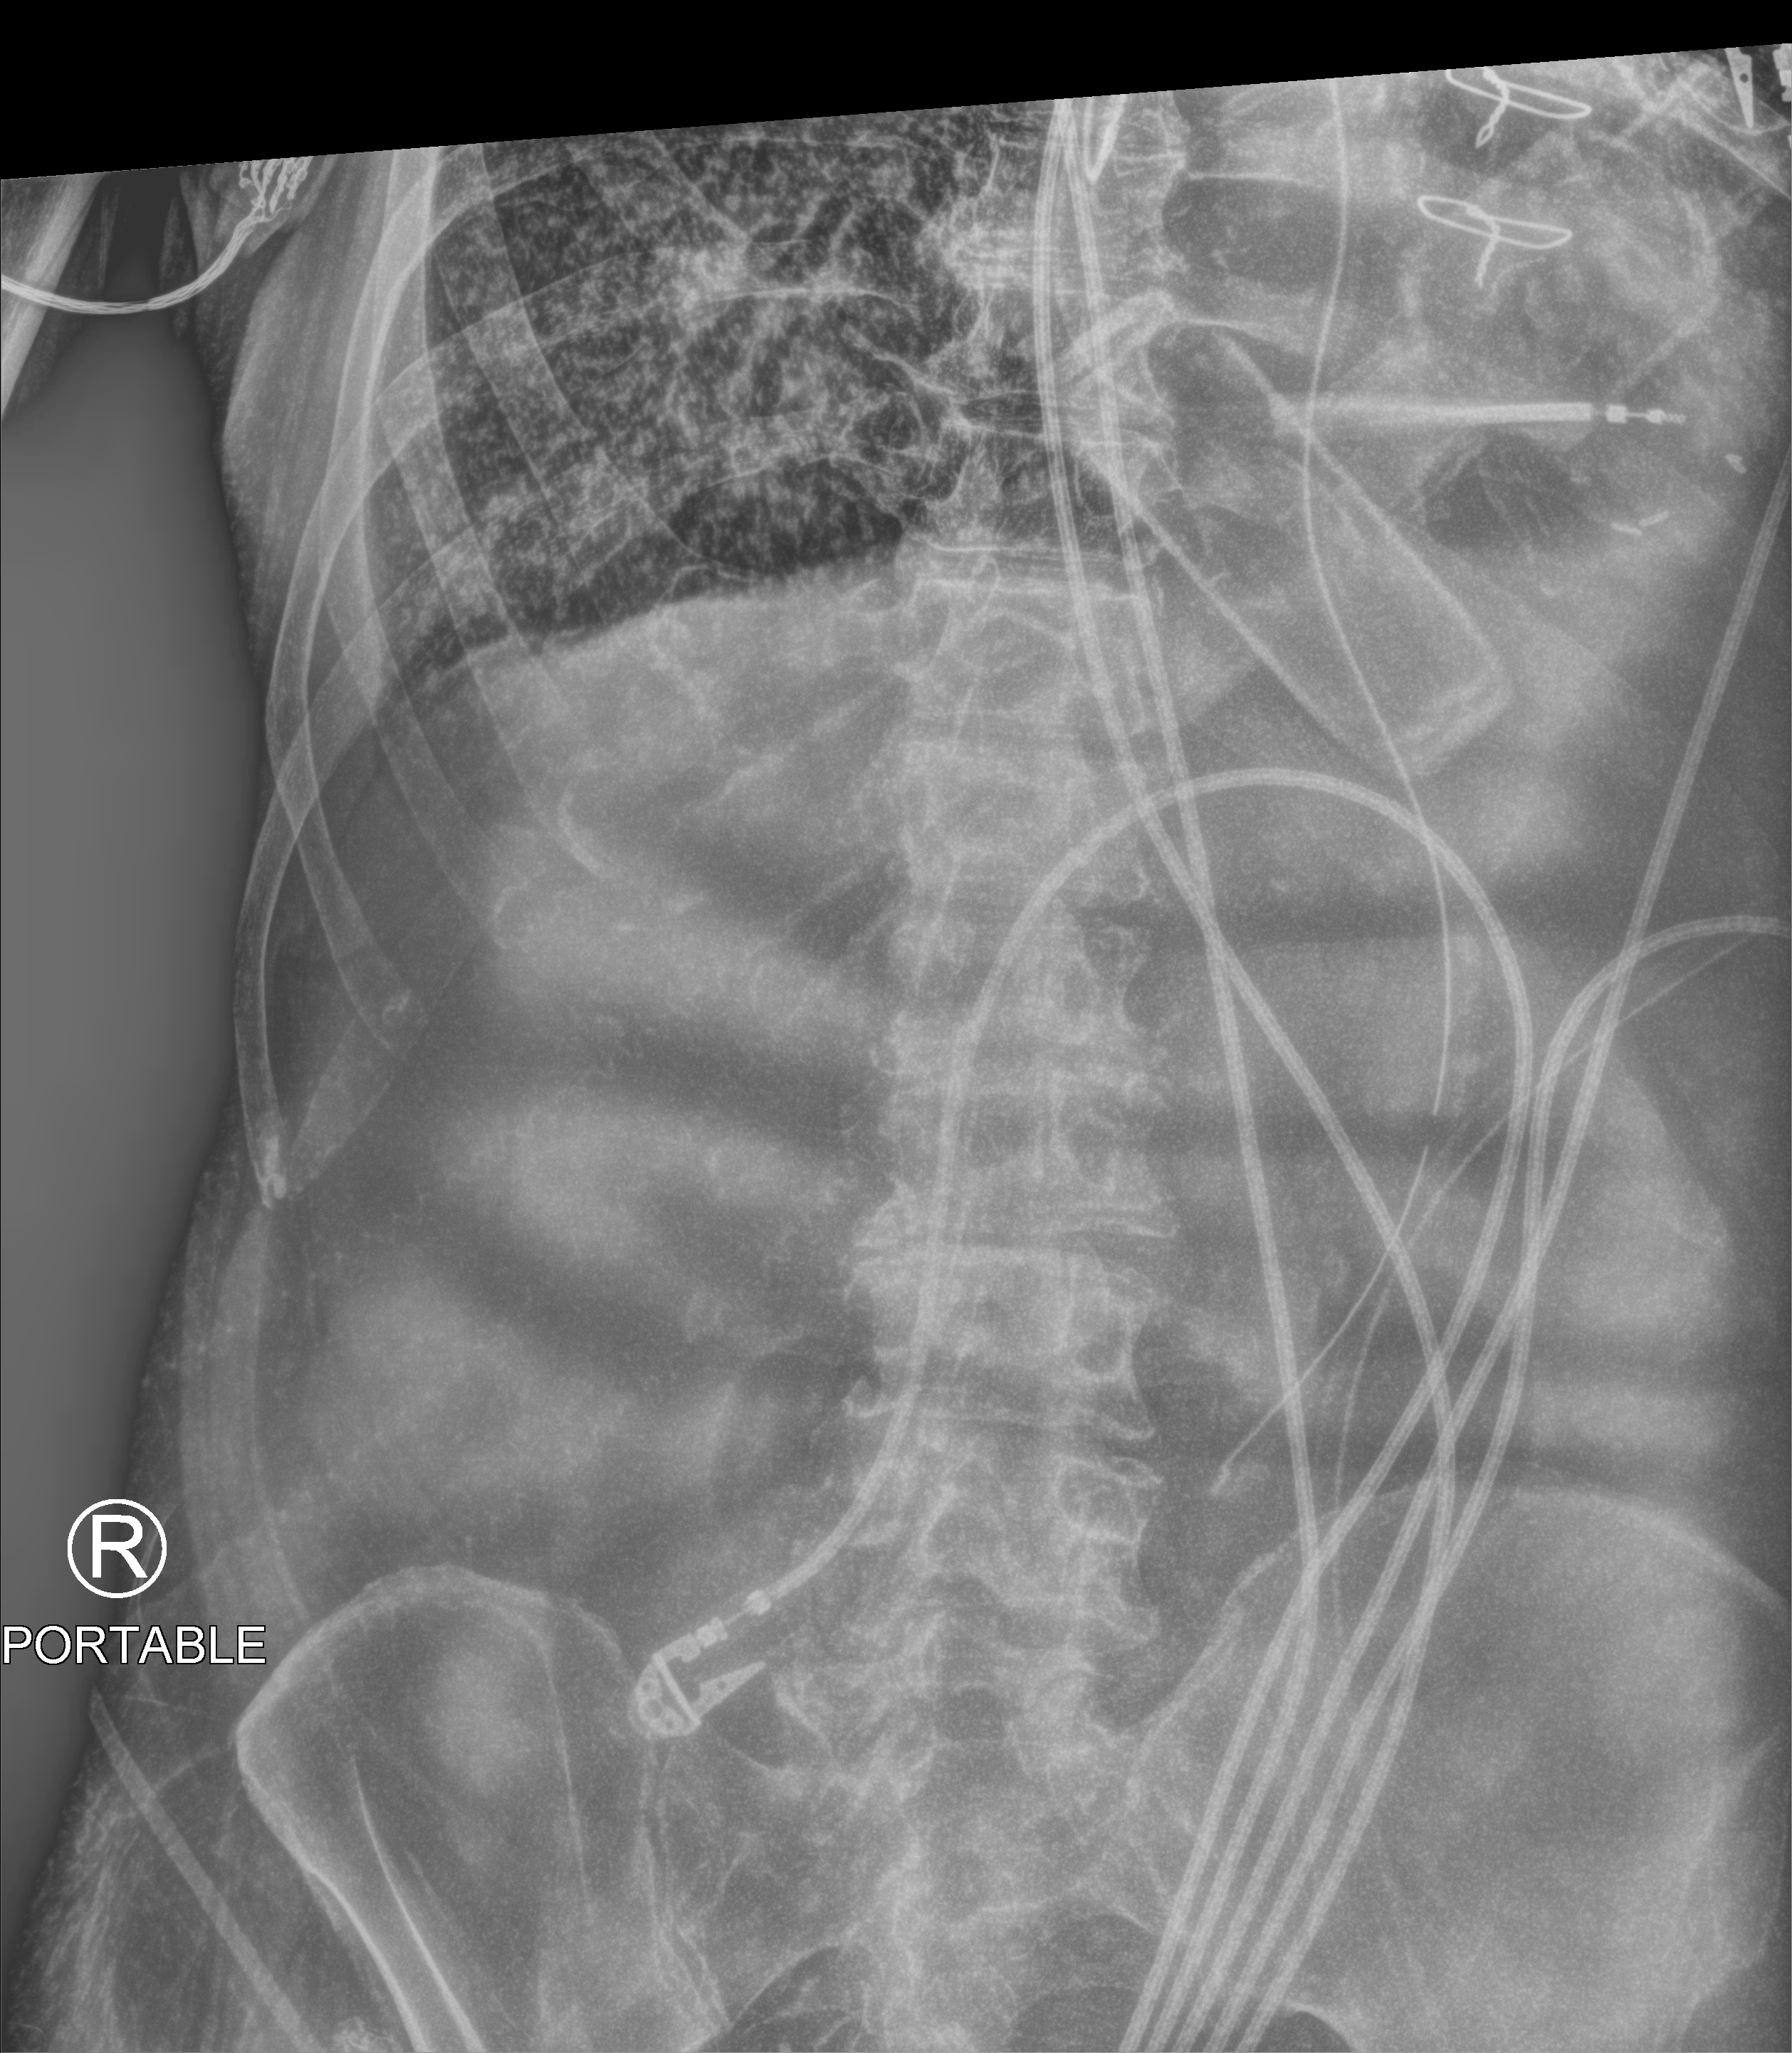
Abdomen X-ray (portable), anteroposterior (AP) projection. Patient hospitalised with COVID-19; male, aged 75–90 years.
From the hospital-stay record, not from the radiograph (when in the stay this image was taken is not recorded):
- admitted to intensive care during this hospital stay: yes